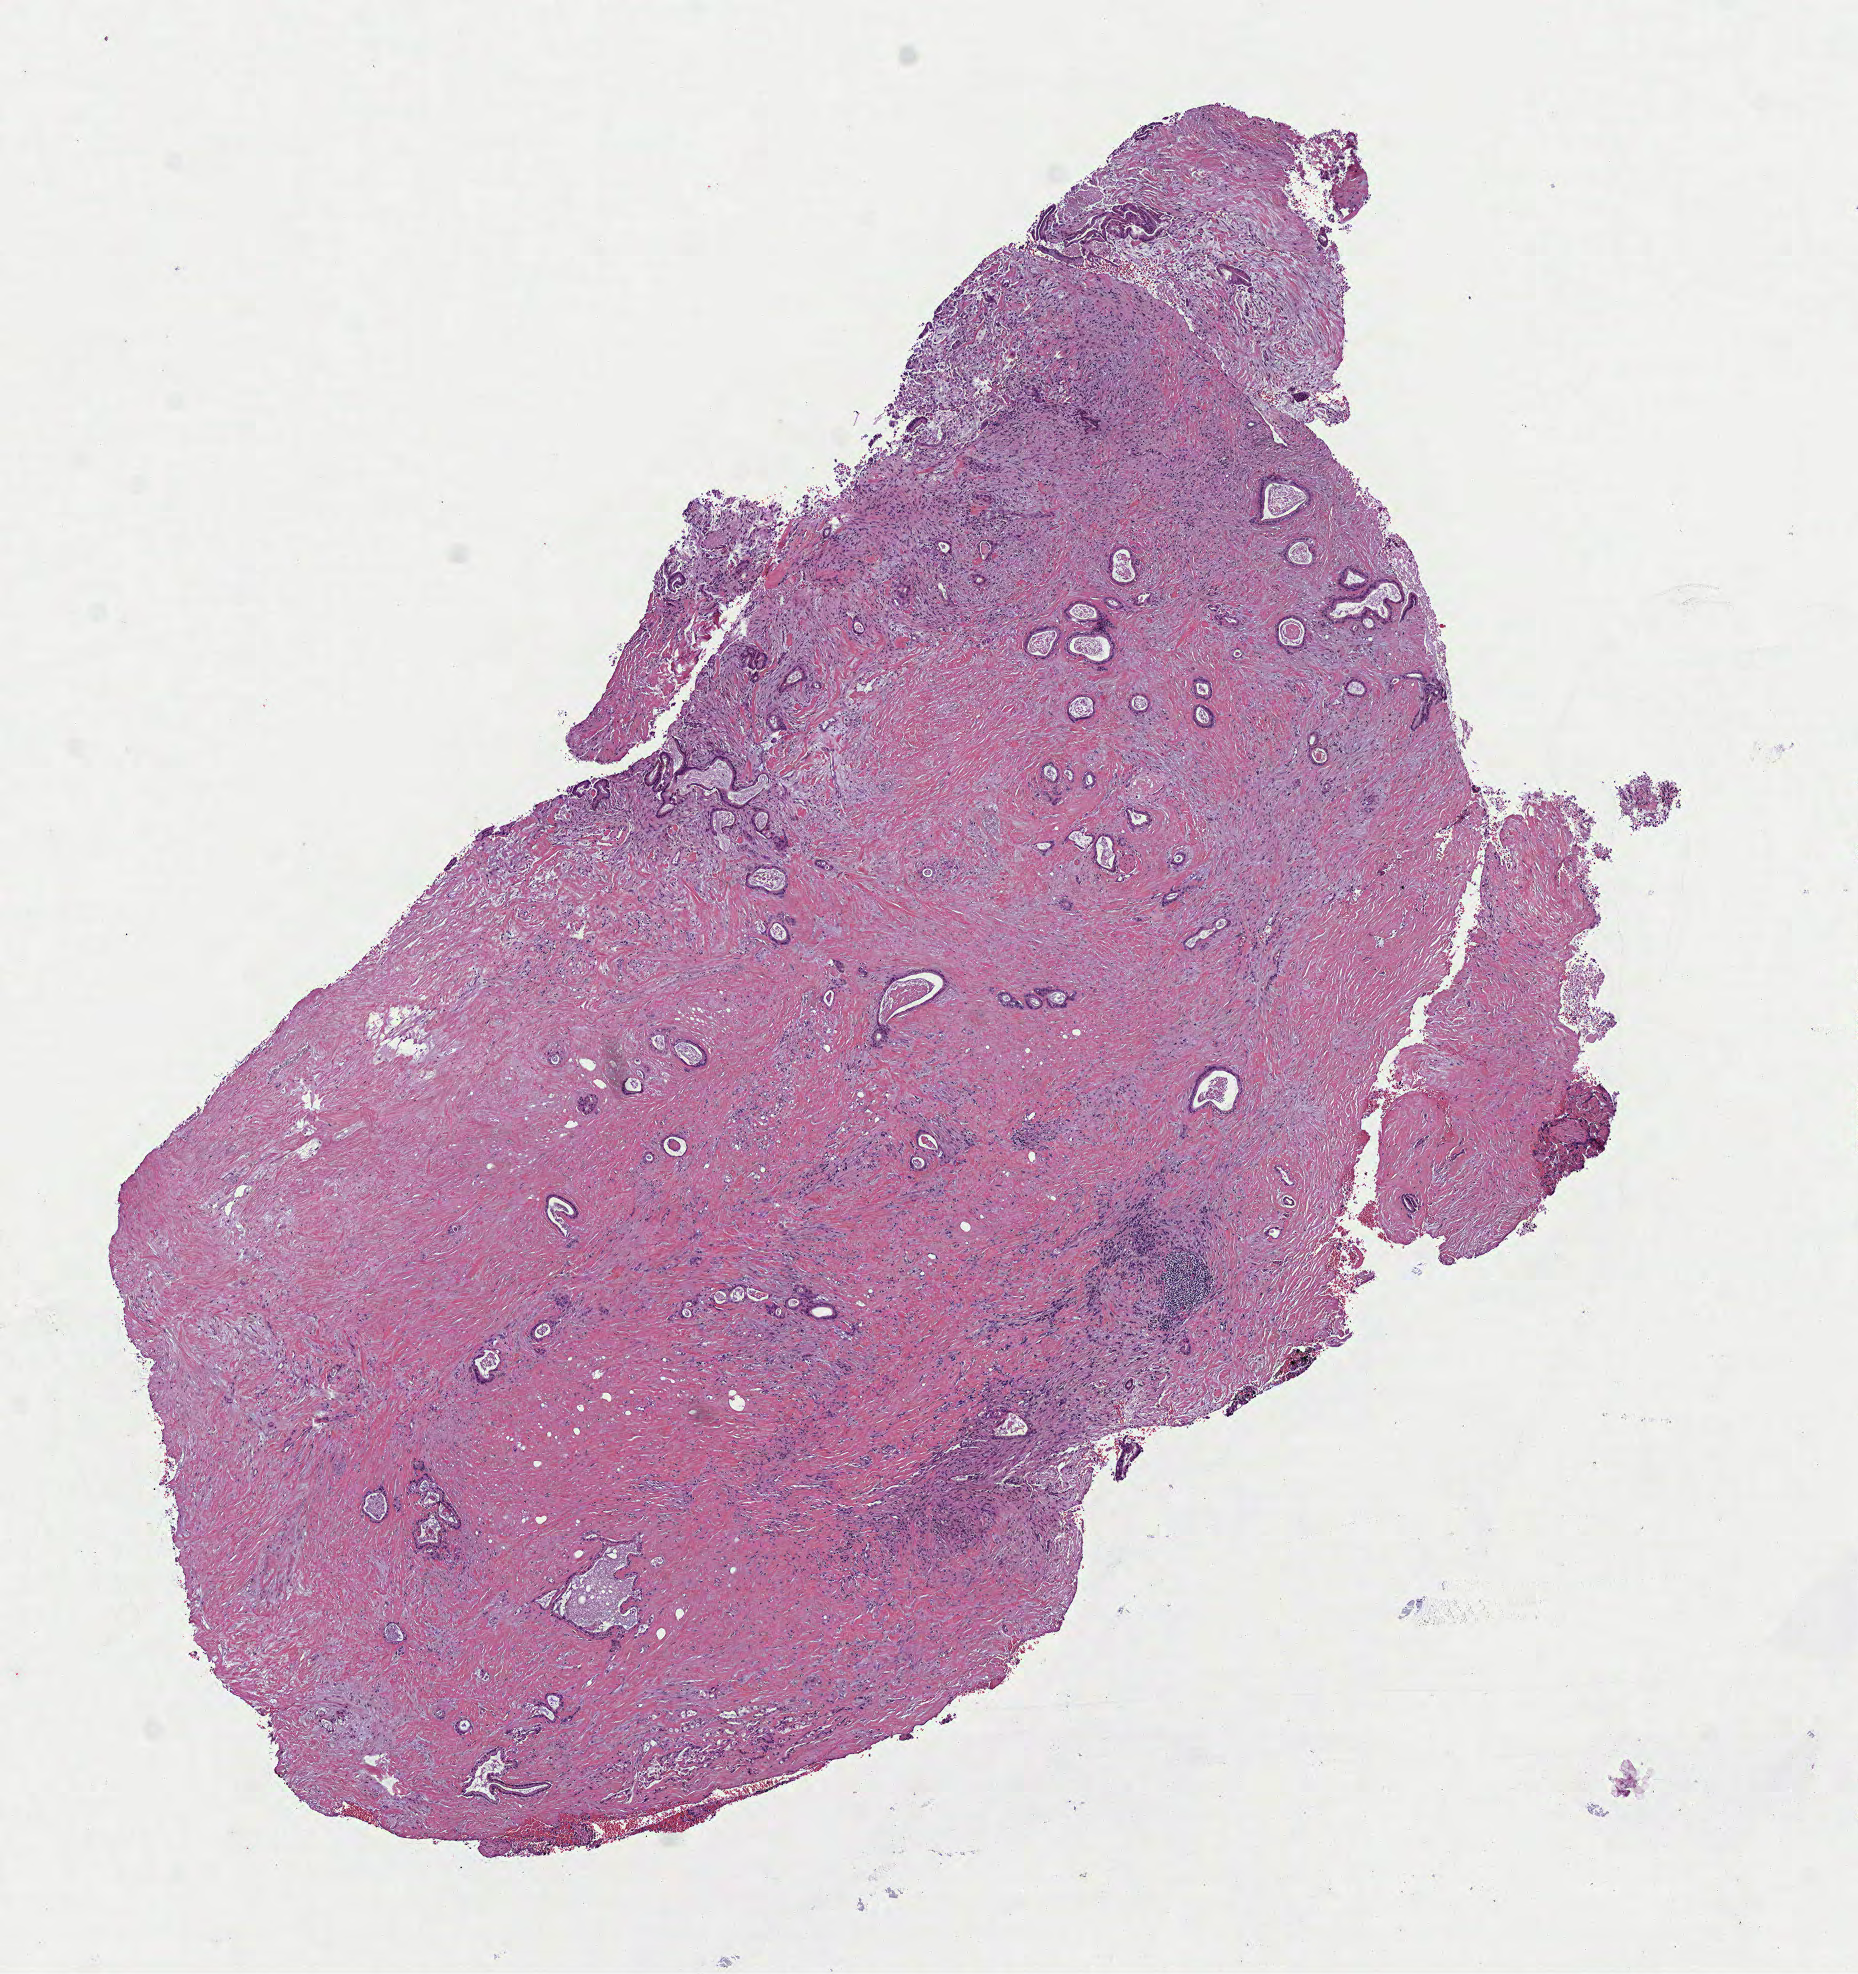
Digitized H&E-stained tissue section (whole slide), a low-resolution overview of the entire scanned area, about 7.5 x 8.0 mm (from a 40x scan); formalin-fixed paraffin-embedded (FFPE) diagnostic section; primary tumour sample from the pancreas. Patient: male, age at initial diagnosis 81 years. Histologic grade: G1 (well differentiated).
- AJCC pathologic stage: IB (7th edition)
- lymph nodes positive (case pathology): 0 of 5 examined
- pathologic diagnosis: Infiltrating duct carcinoma, NOS